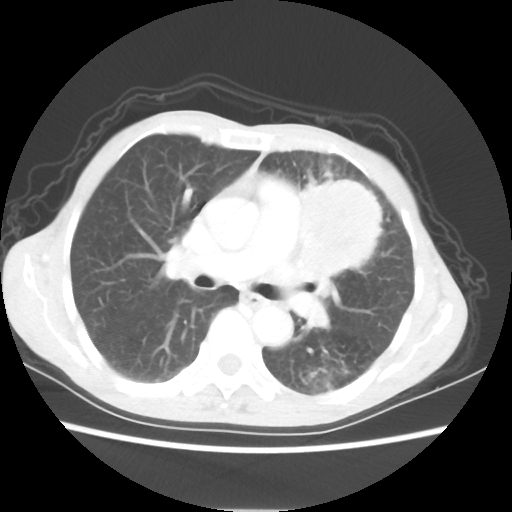
Chest CT, one axial slice; slice 35 of 56 in the series (ordered by position); 80 kVp; lung window (W 1500 / L -600 HU); 512 × 512 image matrix, field of view 331 × 331 mm. Patient: female, 60 years. From the clinical record (not read from this slice): clinical TNM (as recorded): T4 N1 M0.
Structures marked on this image (rectangle marked by the reading radiologist):
- lung tumour (recorded histology: adenocarcinoma): bounding box <296,171,389,285> (left, top, right, bottom; pixels)